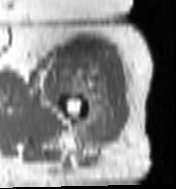
MRI of an extremity soft-tissue mass, one axial slice. Position 87 of 100 along the scan axis. MR volume resampled by the dataset authors to the PET/CT grid (not the native acquisition matrix). 176 × 189 image matrix, field of view 172 × 185 mm. Female patient. Case-level facts recorded for this patient, not image findings: histological type: undifferentiated – high grade; grade: high; site of the primary tumour: left thigh.
Outlined on this slice (expert contour drawn on MRI and transferred to this co-registered scan by the dataset authors):
- gross tumour volume including surrounding oedema: box from (x=71, y=64) to (x=115, y=143) px
- gross tumour volume (mass): (x=78, y=64)–(x=113, y=142)